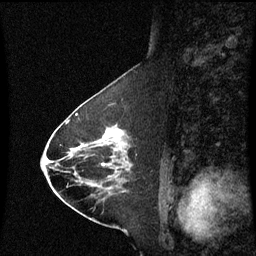
Breast MRI (dynamic contrast-enhanced), one sagittal slice. Dynamic contrast-enhanced series, image 2 of 3 at this slice position (ordered by acquisition). 1.5 T. TE 4.2 ms, TR 8.9 ms. 256 × 256 image matrix. Female patient, age 63 years. From the clinical record (not read from this slice): setting: breast cancer imaged before/during neoadjuvant chemotherapy; receptor status: HR-positive, HER2-negative.
Annotated regions visible in this slice (semi-automatically segmented with operator editing):
- analysis volume of interest (the breast-tissue region the enhancement analysis was run in; not a lesion): bounding box [x1, y1, x2, y2] px = [94, 124, 133, 177]
- tumour enhancement mask (voxels above the 70 % enhancement threshold inside the analysis volume of interest): [106, 132, 125, 137]